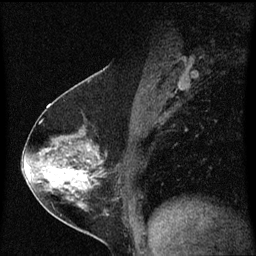
Breast MRI (dynamic contrast-enhanced), one sagittal slice; slice 32 of 60 in the series (ordered by position); dynamic contrast-enhanced series, image 2 of 3 at this slice position (ordered by acquisition); 1.5 T; TE 4.2 ms, TR 8.4 ms; 2 mm slice thickness; 256 × 256 image matrix. Female patient, age 54 years. Case-level facts recorded for this patient, not image findings: setting: breast cancer imaged before/during neoadjuvant chemotherapy; receptor status: HER2-positive.
Annotated regions visible in this slice (semi-automatic segmentation, software-assisted and operator-edited):
- analysis volume of interest (the breast-tissue region the enhancement analysis was run in; not a lesion): bounding box <32,122,121,213> (left, top, right, bottom; pixels)
- tumour enhancement mask (voxels above the 70 % enhancement threshold inside the analysis volume of interest): <48,170,89,181>